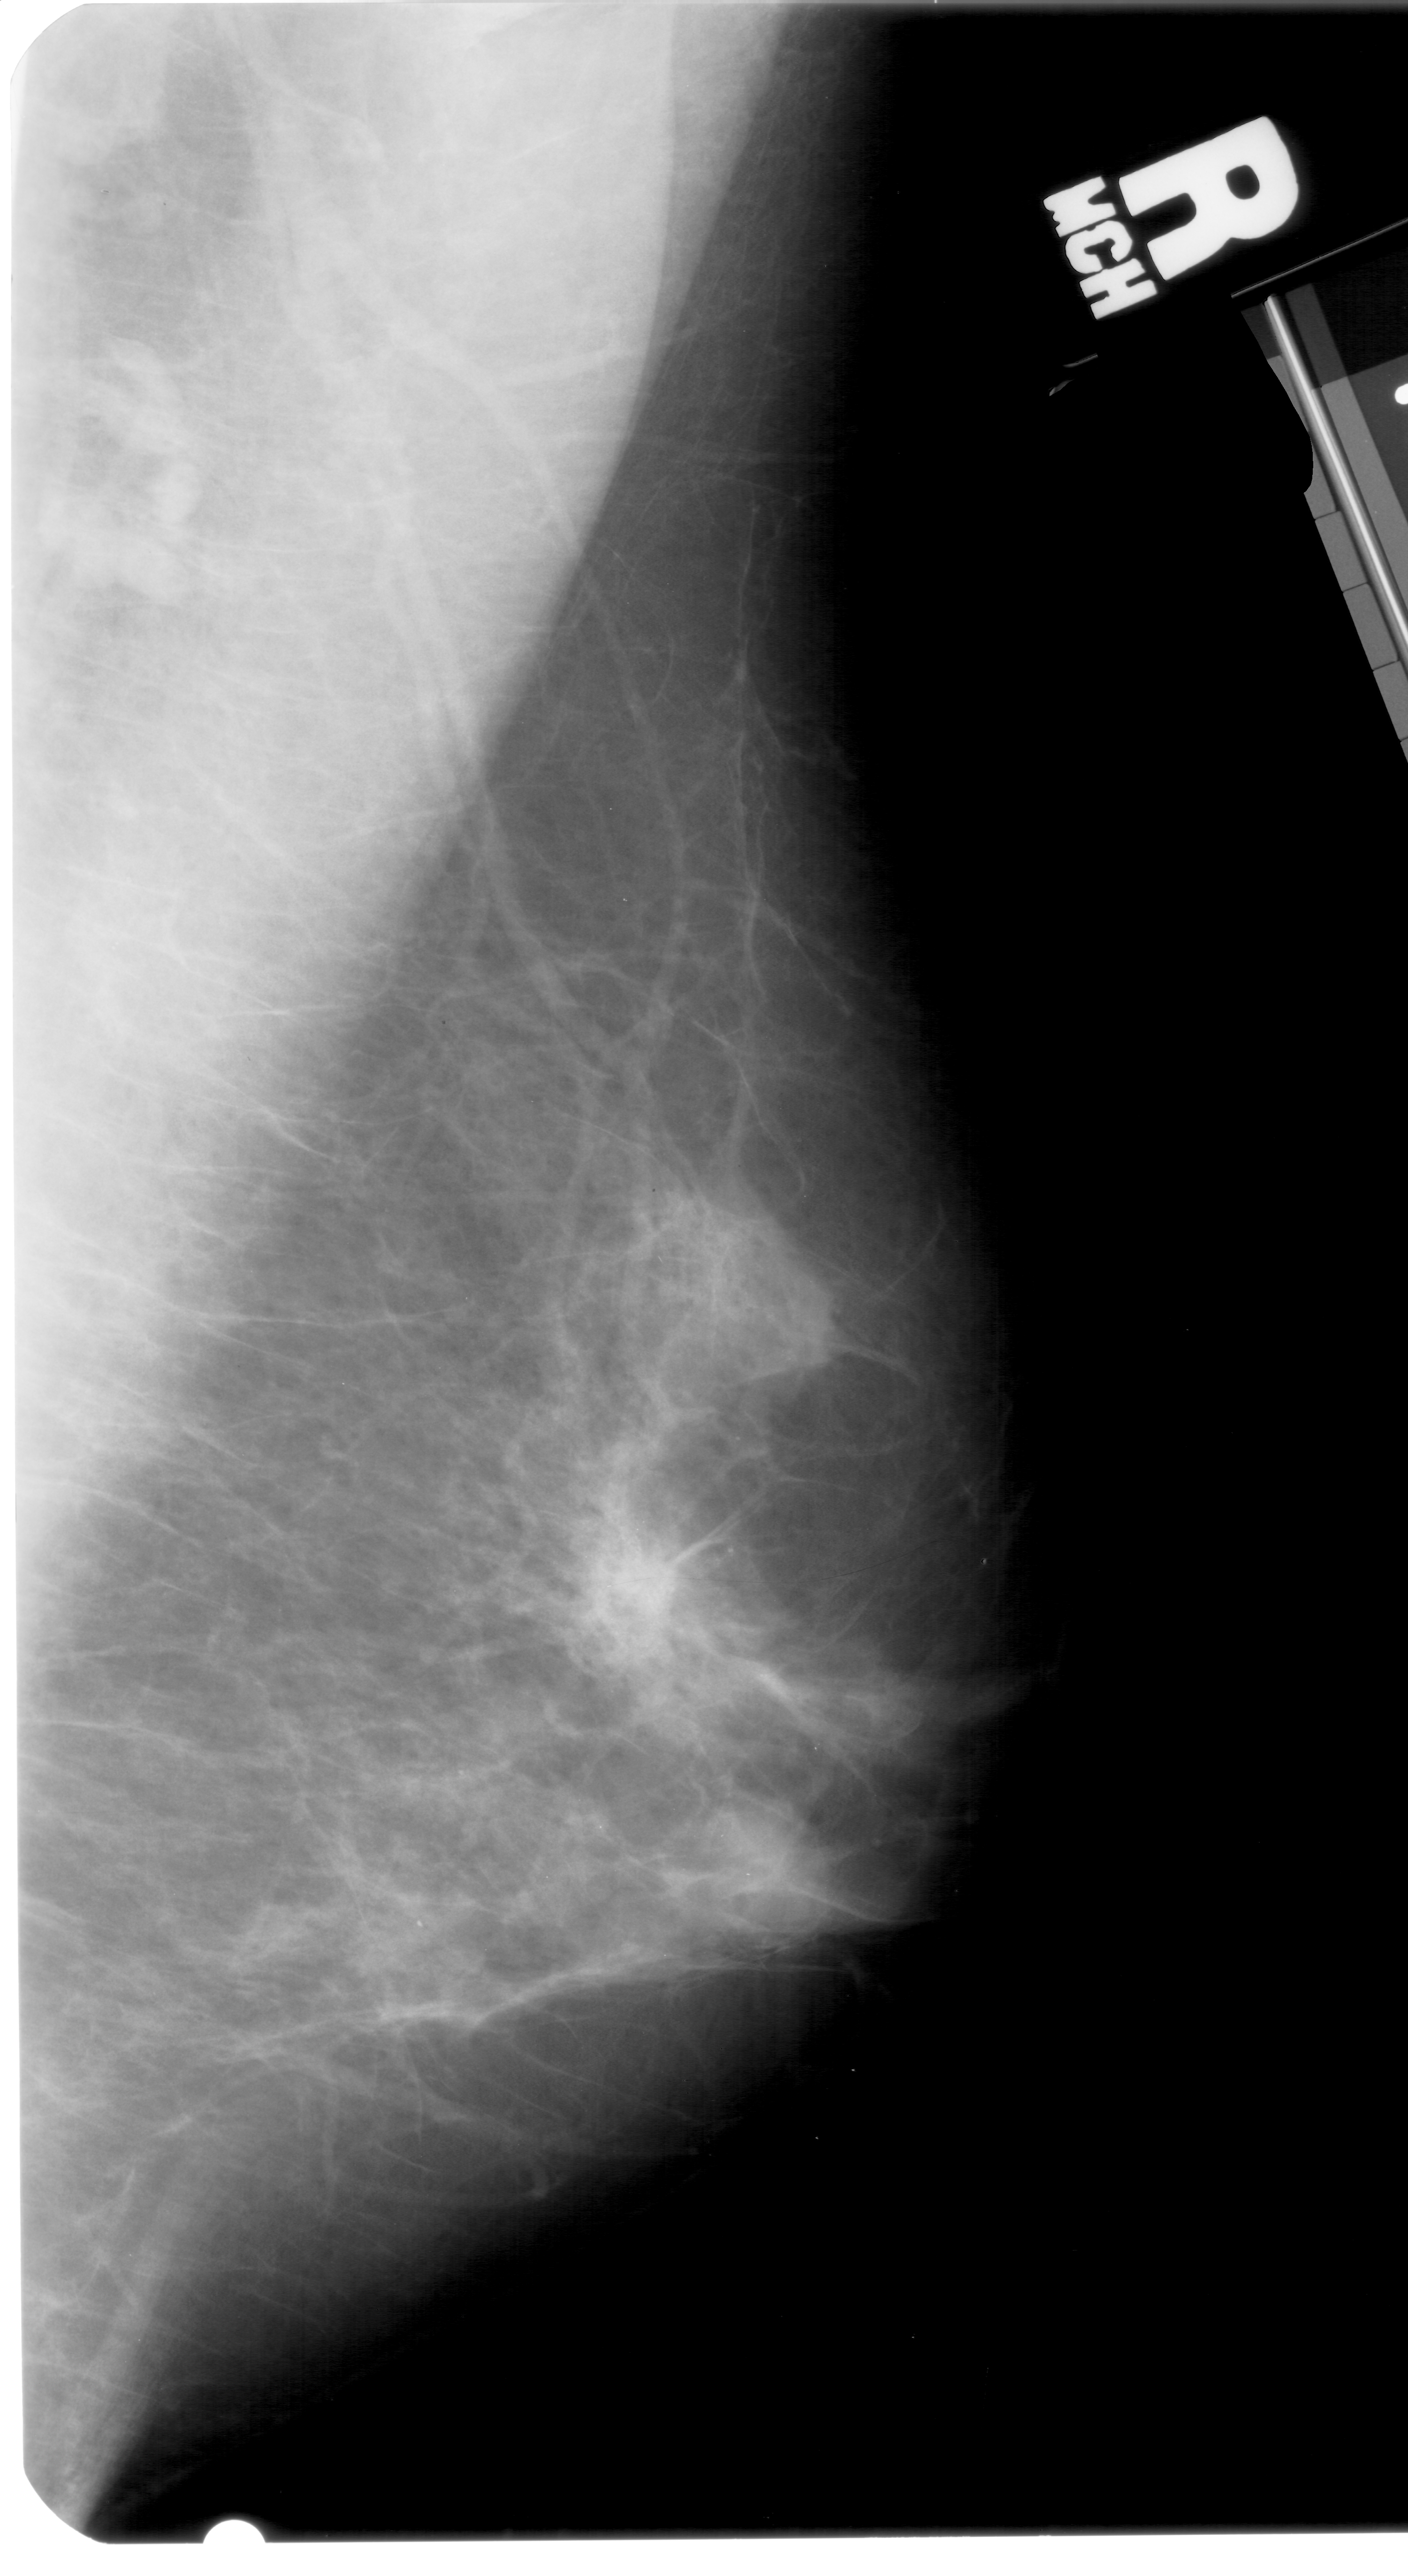
Digitized screen-film mammogram; right breast; mediolateral oblique (MLO) view.
Marked abnormality: calcifications, morphology pleomorphic, distribution clustered; BI-RADS assessment category 4; subtlety rating 3 on a 1 (subtle) to 5 (obvious) scale; pathology result (as recorded, not read from the image): malignant.